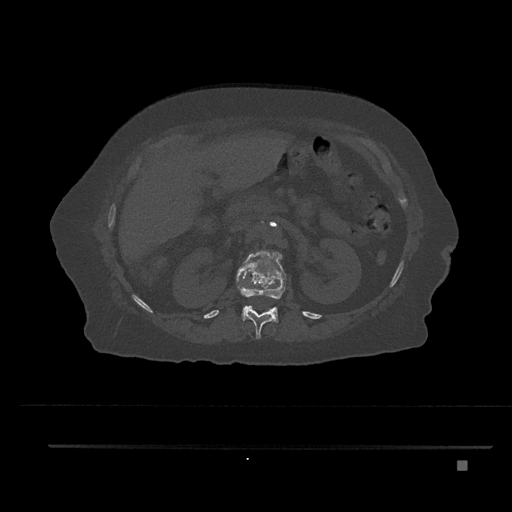
CT including the spine, one axial slice. Position 241 of 797 along the scan axis. 120 kVp. Bone window (W 1800 / L 400 HU). 512 × 512 image matrix. Female patient, age 76 years. Case-level facts recorded for this patient, not image findings: primary cancer: lung; vertebrae with lytic lesions (as recorded): T11, L3.
Annotated regions visible in this slice (semi-automatic segmentation, software-assisted and operator-edited):
- L1 vertebra: bounding box [x1, y1, x2, y2] px = [236, 250, 286, 323]
- T12 vertebra: [240, 286, 275, 339]